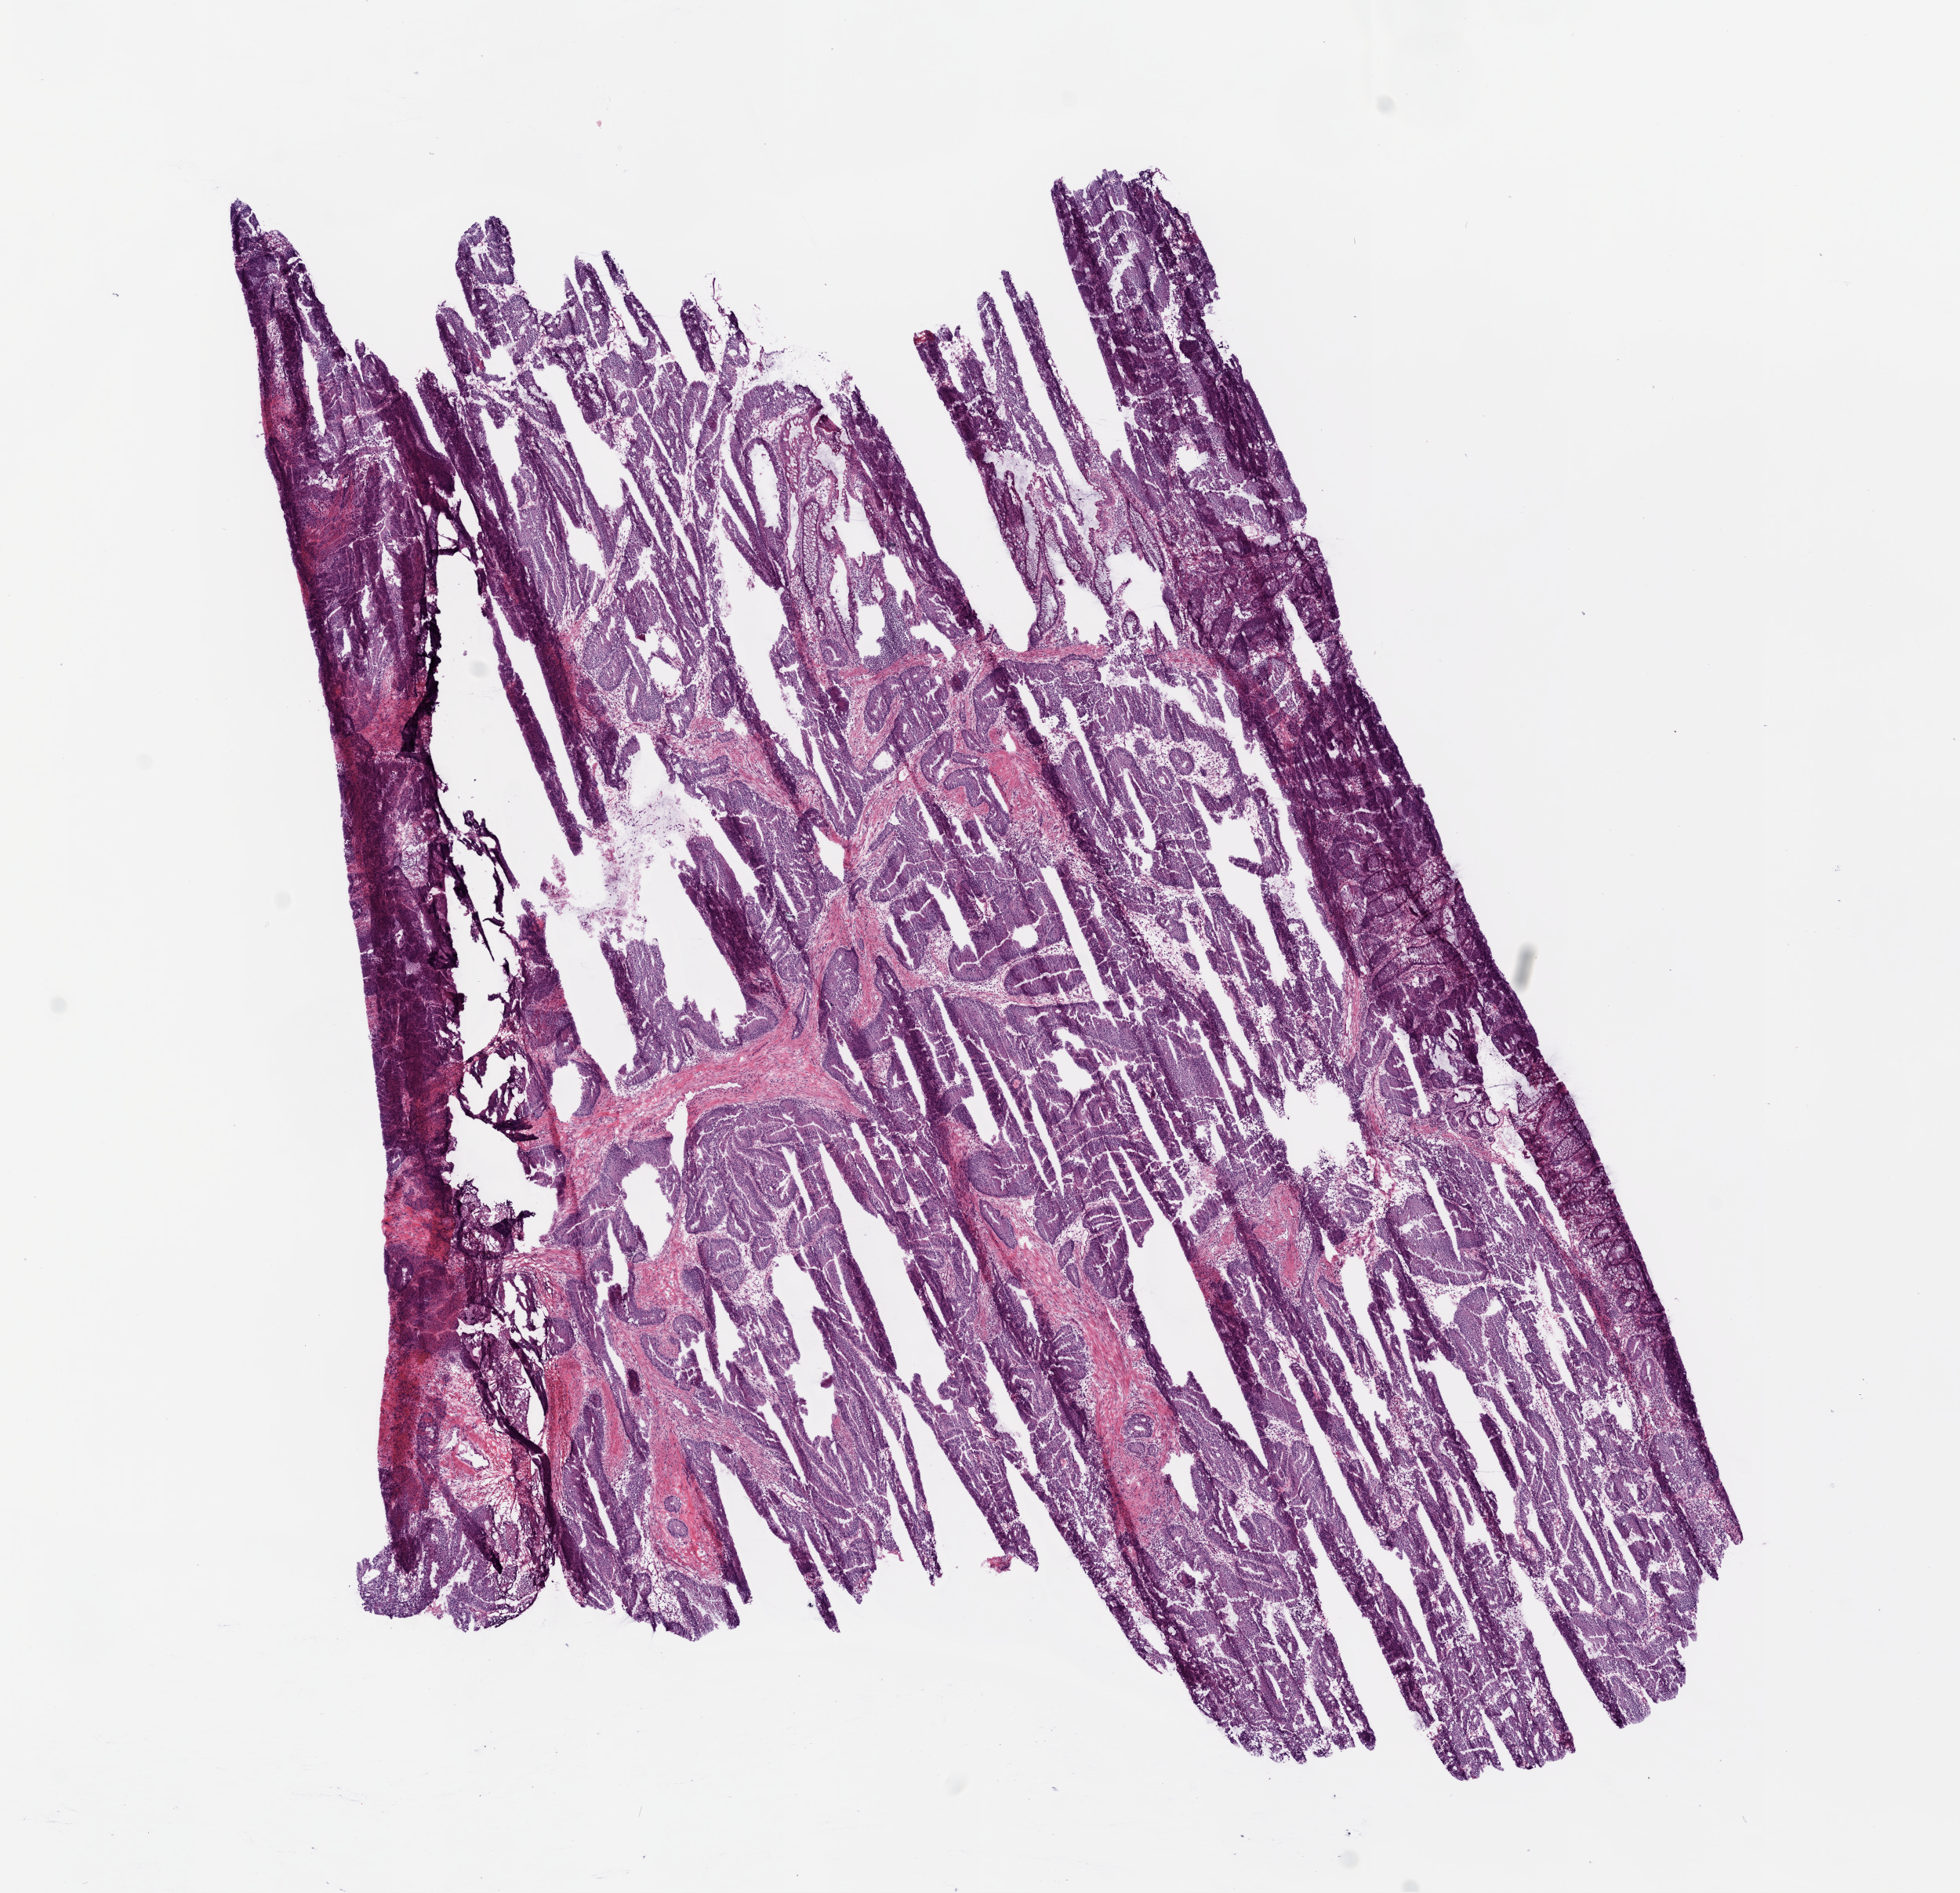
Digitized H&E tissue section (whole slide), shown as a low-resolution overview of the whole scanned area (about 10.0 x 9.7 mm, from a 20x scan); frozen section from the bottom of the tissue portion; colon, primary tumour sample. Female patient; age at initial diagnosis 72 years. Composition of this section per pathologist review: tumour cells 80%, tumour nuclei 90%, normal cells 0%, stromal cells 20%, necrosis 0%.
• pathologic diagnosis: Adenocarcinoma, NOS (sigmoid colon)
• lymph nodes positive (case pathology): 5 of 25 examined
• AJCC pathologic stage: IIIC (6th edition)